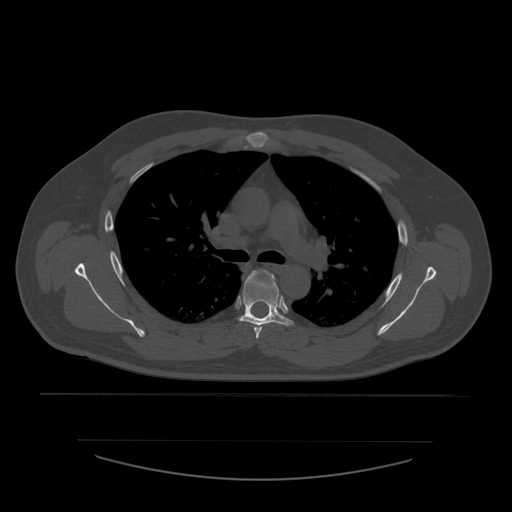
CT including the spine, one axial slice; slice 402 of 532 in the series (ordered by position); reconstruction kernel STANDARD; bone window (W 1800 / L 400 HU); 1.25 mm slice thickness; 512 × 512 image matrix, field of view 441 × 441 mm. Patient age 44 years. From the clinical record (not read from this slice): primary cancer: soft tissue sarcoma.
Outlined on this slice (semi-automatically segmented with operator editing):
- T4 vertebra: bounding box (x1, y1, x2, y2) in pixels: (253, 271, 280, 339)
- T5 vertebra: (239, 270, 294, 327)